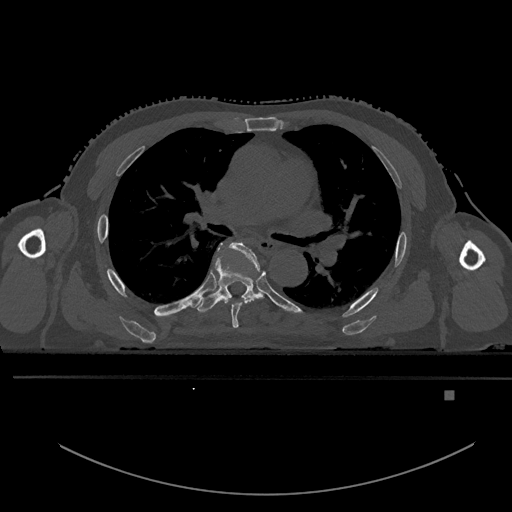
CT including the spine, one axial slice; position 331 of 969 along the scan axis; bone window (W 1800 / L 400 HU); 0.5 mm slice thickness; 512 × 512 image matrix. Patient: male, 82 years. Case-level facts recorded for this patient, not image findings: primary cancer: prostate; vertebrae with lytic lesions (as recorded): T11, T9, T8, T2.
Structures marked on this image (semi-automatic segmentation, software-assisted and operator-edited):
- T5 vertebra: bounding box [x1, y1, x2, y2] px = [221, 242, 262, 328]
- T6 vertebra: [191, 244, 261, 313]